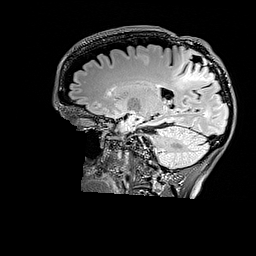
Brain MRI from a brain-tumour surgery series, one sagittal slice. Slice 108 of 176 in the series (ordered by position). T2 FLAIR. 1 mm slice thickness. 256 × 256 image matrix, field of view 256 × 256 mm. Case-level facts recorded for this patient, not image findings: histopathology: Astrocytoma; WHO grade: 3; IDH mutation: yes; tumour location: Right Parietal.
Annotated regions visible in this slice (expert manual segmentation):
- tumour: box from (x=175, y=49) to (x=216, y=87) px
- tumour: (x=185, y=59)–(x=214, y=83)